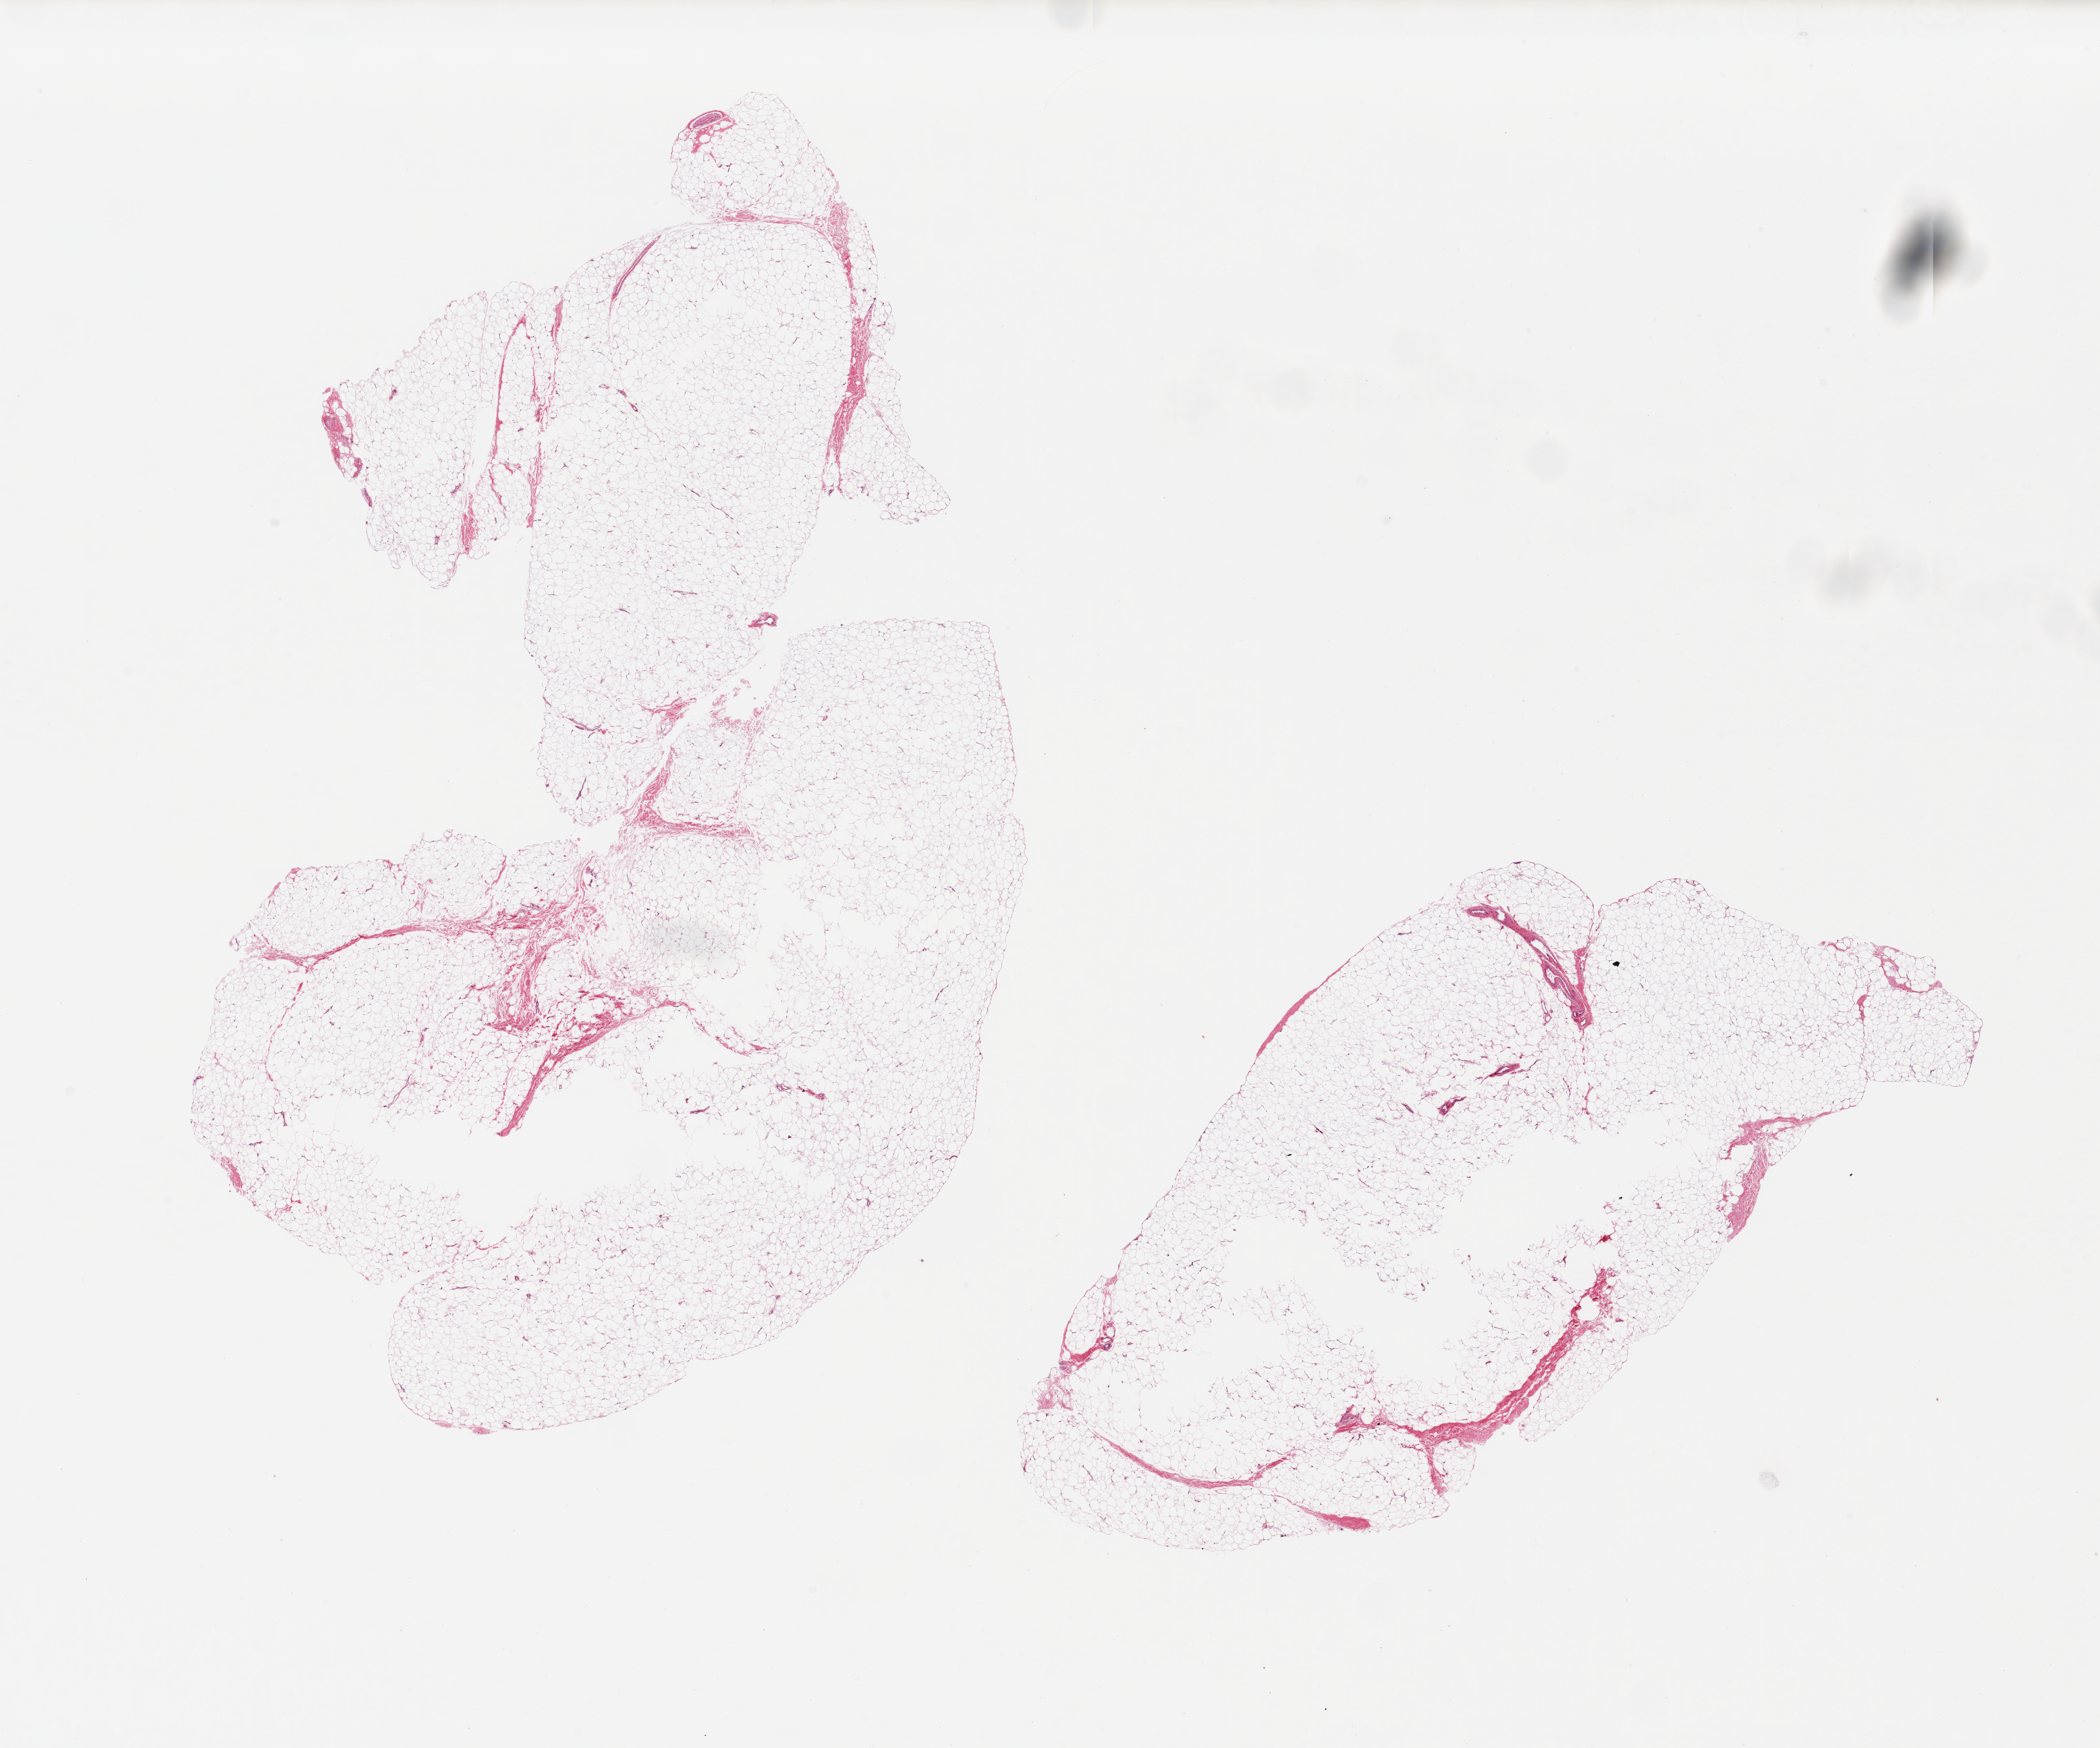
Whole-slide image, H&E stain — a low-resolution overview of the entire scanned area, about 24.6 x 20.5 mm (slide scanned at 20x); PAXgene-fixed, paraffin-embedded tissue; target tissue: breast; donor tissue sample. Male donor.
- review note (as recorded): 2 pieces, ~13x7mm, all fibroadipose, no ductal elements noted